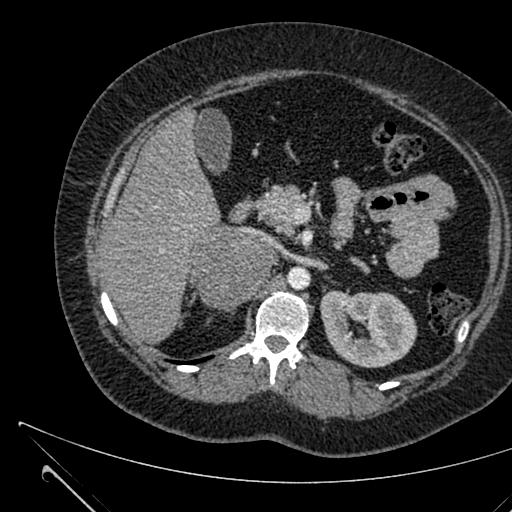
Contrast-enhanced abdominal CT, one axial slice. Position 398 of 731 along the scan axis. 120 kVp. Intravenous contrast given. Soft-tissue window (W 400 / L 40 HU). 1 mm slice thickness. 512 × 512 image matrix, field of view 376 × 376 mm. Female patient, age 36 years. From the clinical record (not read from this slice): diagnosis: adrenocortical carcinoma; tumour side: right adrenal; tumour size at pathology: 10 cm; Ki-67 index: 20 %; stage (as recorded): 4.
Outlined on this slice (semi-automatically segmented with operator editing):
- mass: bounding box [x1, y1, x2, y2] px = [193, 230, 271, 309]